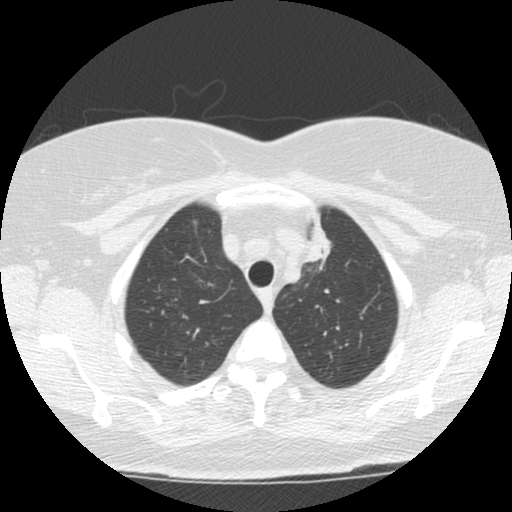
Low-dose screening chest CT, one axial slice; slice 98 of 120 in the series (ordered by position); reconstruction kernel STANDARD; lung window (W 1500 / L -600 HU); 512 × 512 image matrix, field of view 310 × 310 mm.
Annotated regions visible in this slice (manually delineated by an expert):
- lesion 1 (tumor, upper lobe of left lung): box from (x=304, y=214) to (x=331, y=263) px